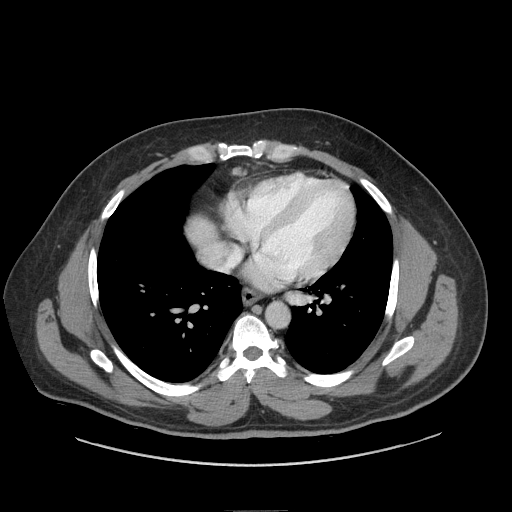
Contrast-enhanced abdominal CT (liver protocol), one axial slice; slice 80 of 87 in the series (ordered by position); reconstruction kernel STANDARD; 140 kVp; soft-tissue window (W 400 / L 40 HU); 2.5 mm slice thickness; 512 × 512 image matrix. From the clinical record (not read from this slice): diagnosis: hepatocellular carcinoma (patient treated with transarterial chemoembolisation; whether this scan precedes or follows treatment is not stated here); TNM stage (as recorded): Stage-II; Child-Pugh class: A; tumour differentiation: moderately differentiated.
Annotated regions visible in this slice (semi-automatic segmentation, software-assisted and operator-edited):
- liver parenchyma outside the tumour (the mass and vessels are separate outlines, so this box may not span the whole liver): bounding box <188,218,212,240> (left, top, right, bottom; pixels)